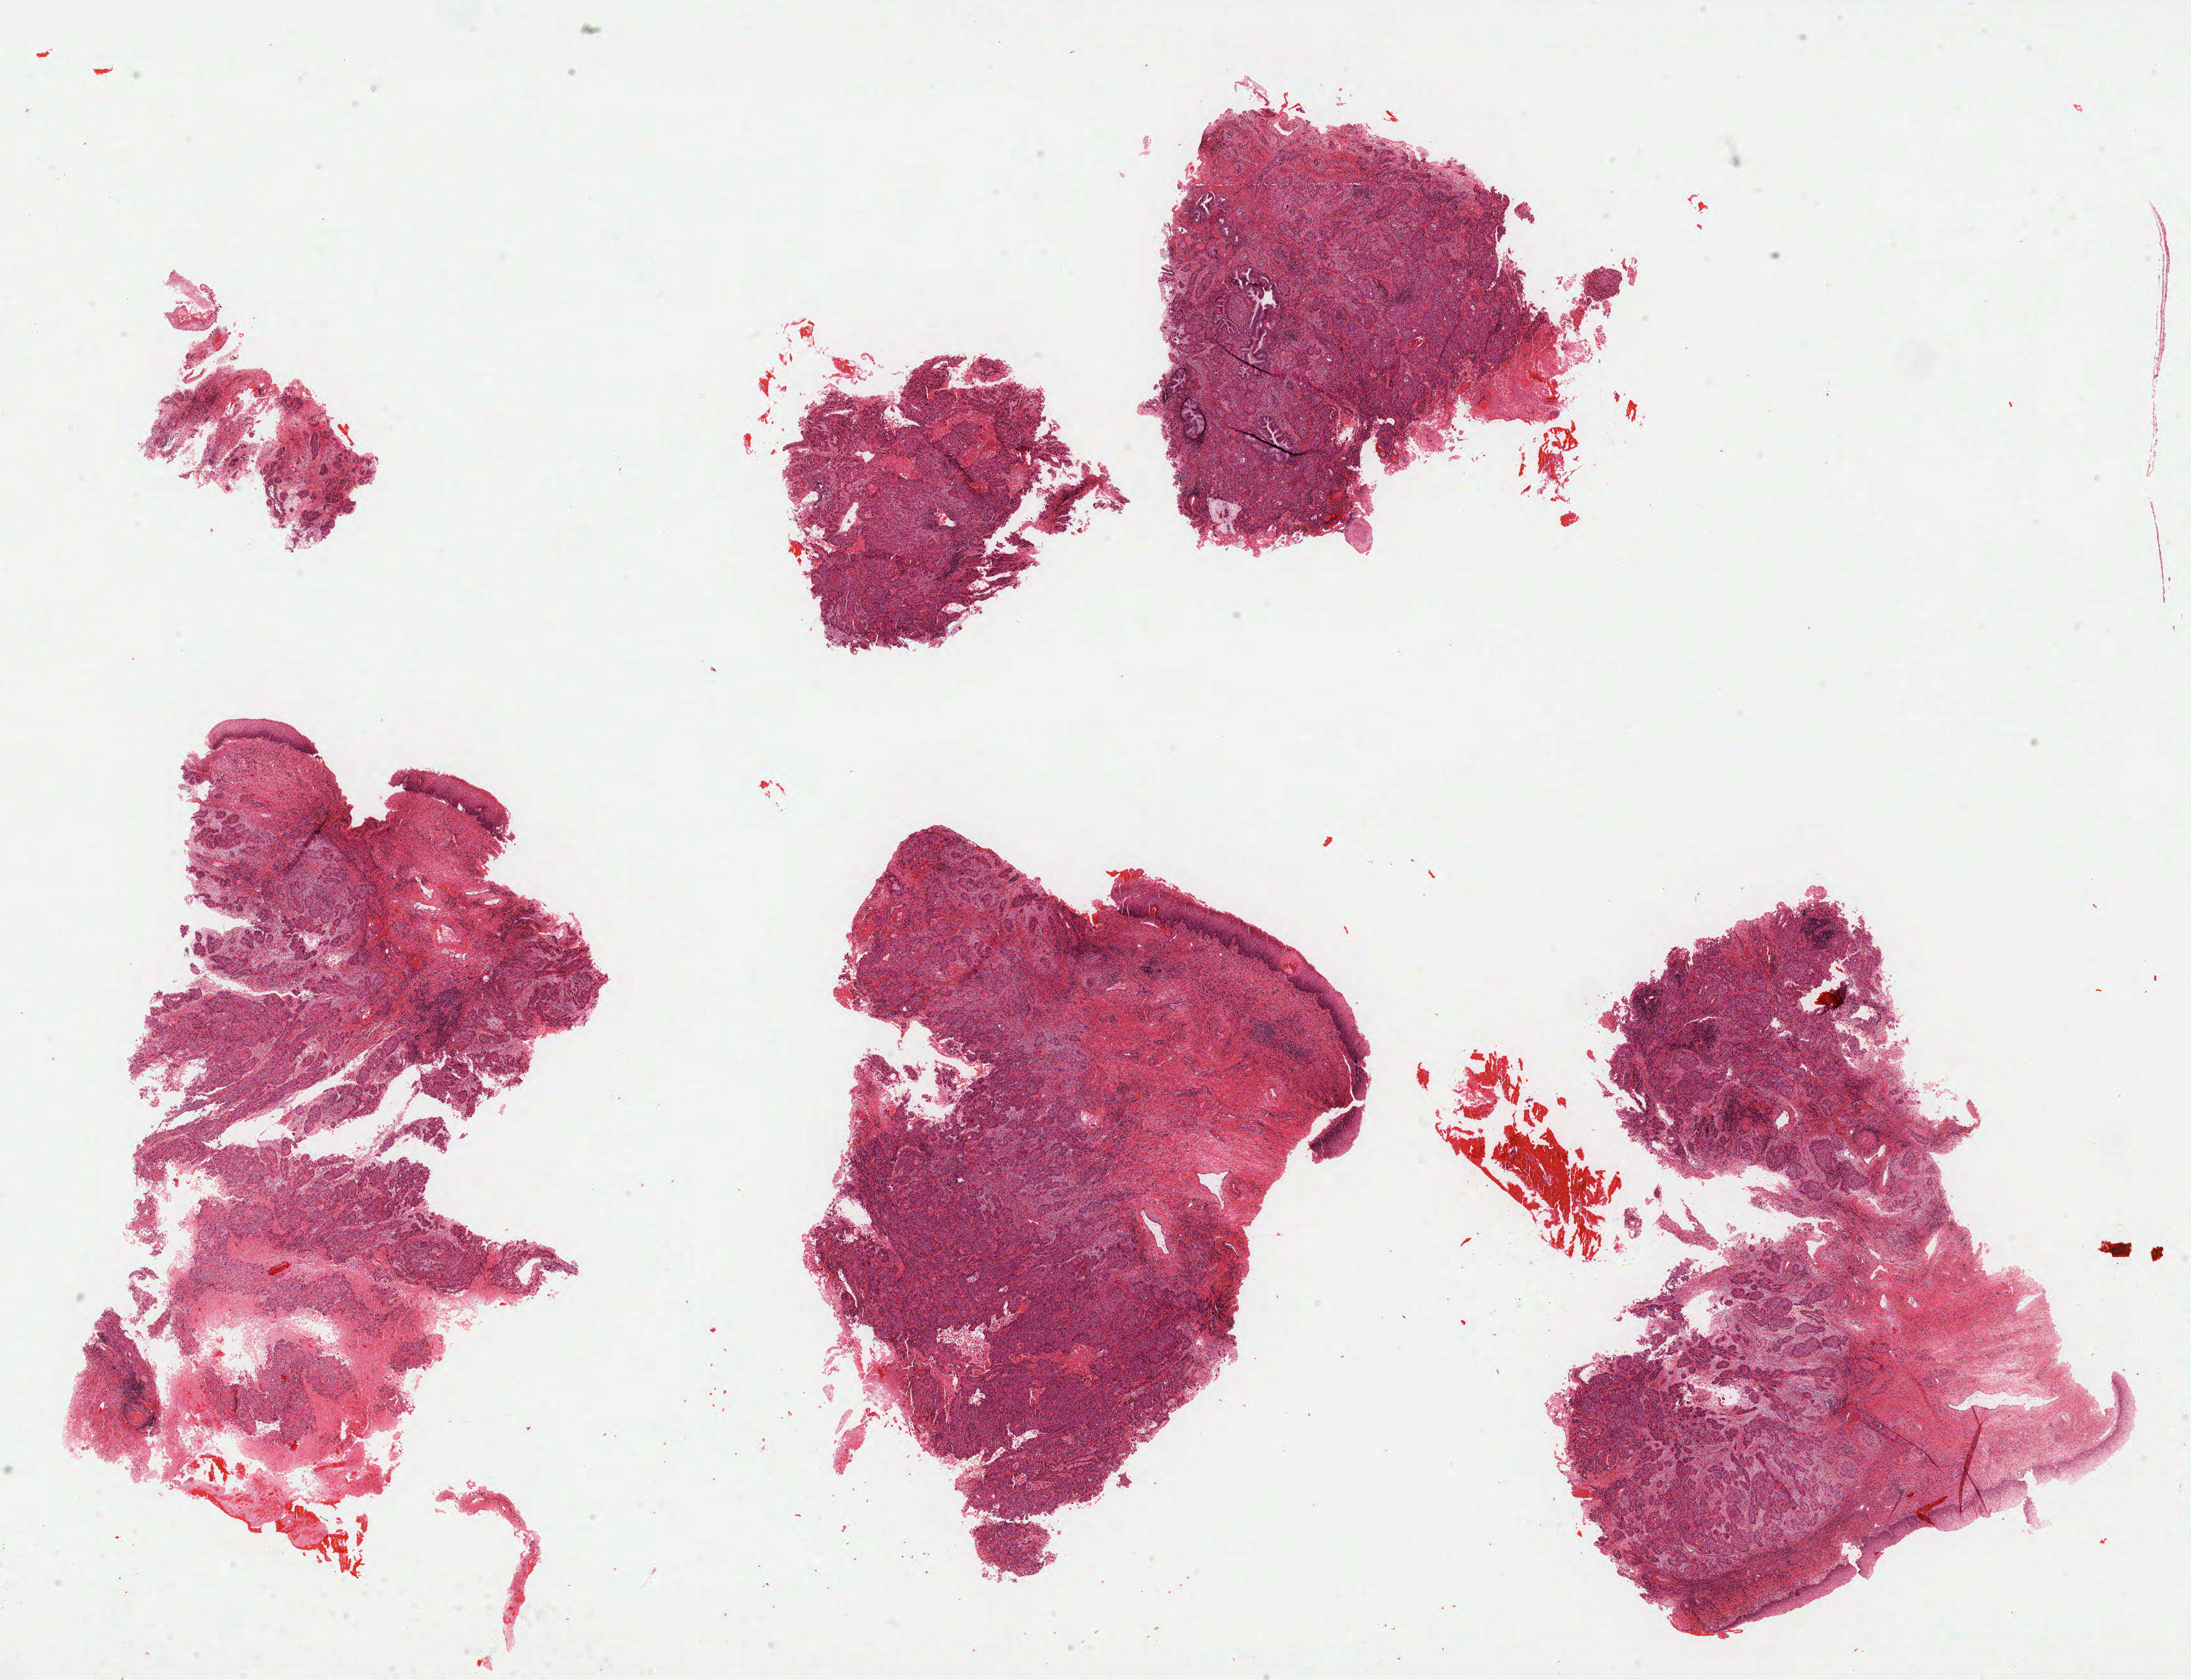
Digitized Hematoxylin and eosin (H&E) stained tissue section (whole slide) — a low-resolution overview of the entire scanned area, about 27.4 x 21.0 mm (acquisition: 40x scan), formalin-fixed paraffin-embedded (FFPE) diagnostic section, primary tumour sample from the cervix. Female patient; age at initial diagnosis 42 years. Histologic grade: G2 (moderately differentiated).
FIGO stage: IIIB. Pathologic diagnosis: Squamous cell carcinoma, NOS (cervix uteri).